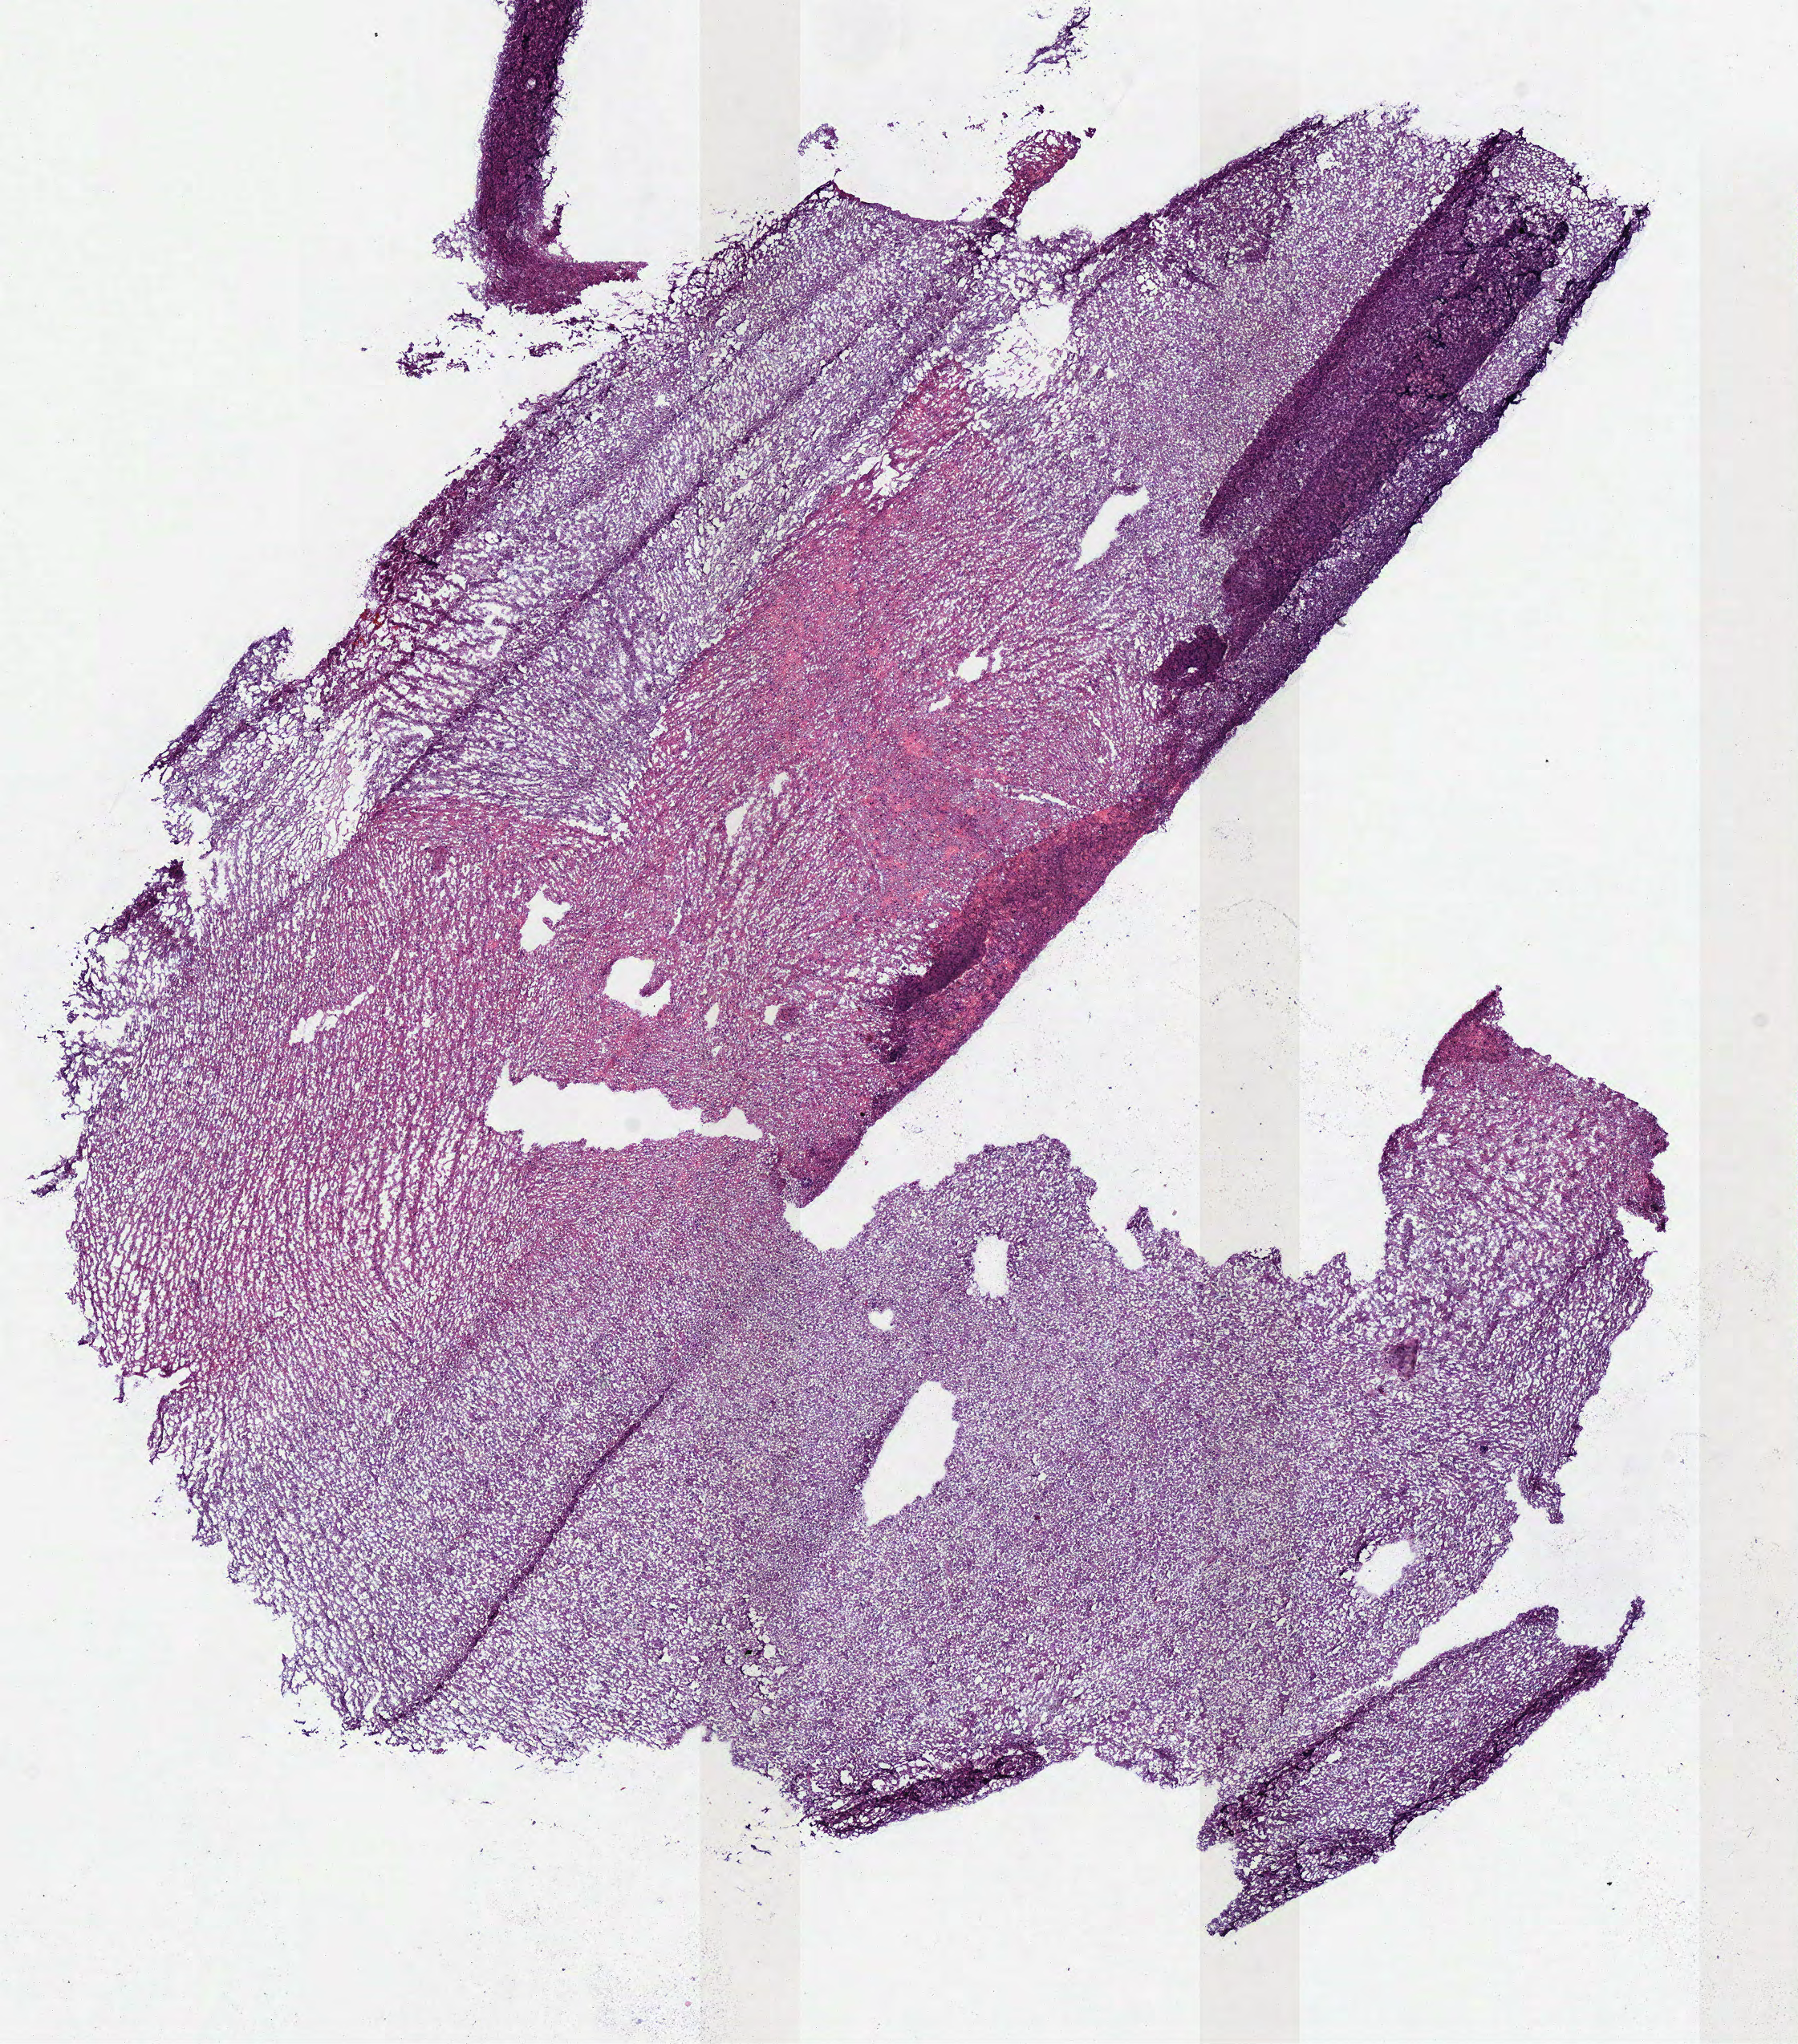
Whole-slide histology image, Hematoxylin and eosin (H&E) stained, whole scanned area (about 8.8 x 10.0 mm) shown as a low-resolution overview, frozen section from the top of the tissue portion, sample: primary tumour, brain. Female patient; age at initial diagnosis 32 years. Histologic grade: G2 (moderately differentiated). Pathologist review of this section (percent, as recorded): tumour cells 100%, tumour nuclei 70%, normal cells 0%, stromal cells 0%, necrosis 0%.
Diagnosis: Oligodendroglioma, NOS (cerebrum). Laterality: left.